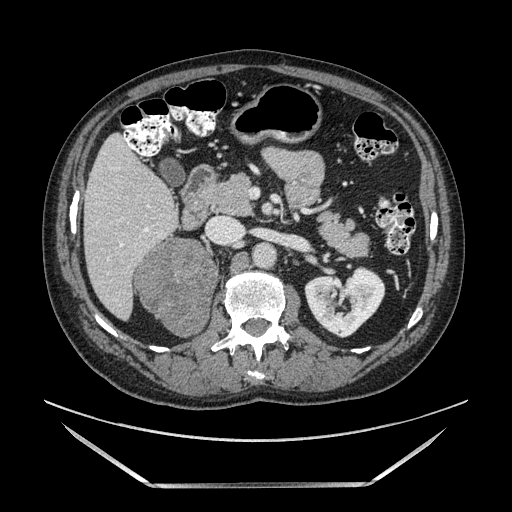
Contrast-enhanced abdominal CT, one axial slice; position 64 of 185 along the scan axis; soft-tissue window (W 400 / L 40 HU); 1.25 mm slice thickness; 512 × 512 image matrix. Male patient. From the clinical record (not read from this slice): diagnosis: adrenocortical carcinoma; tumour side: right adrenal; tumour size at pathology: 10.3 cm; Ki-67 index: 20 %; stage (as recorded): 3.
Annotated regions visible in this slice (semi-automatic segmentation, software-assisted and operator-edited):
- mass: box from (x=136, y=240) to (x=217, y=335) px